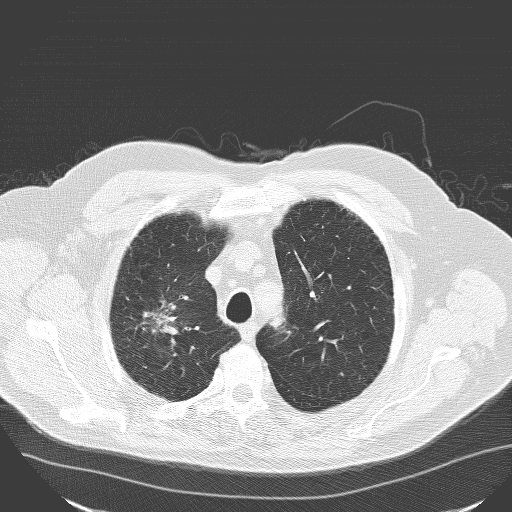
Low-dose screening chest CT, axial slice. First (baseline) screen. Lung window (W 1500 / L -600 HU). 3.2 mm slice thickness. 120 kVp. Slice 131 of 160 in the series. 512 × 512 image matrix. Male, age 71 years at enrolment. Current smoker at enrolment.
Expert-annotated lung lesion, bounding box (x1, y1, x2, y2) in pixels: (114, 277, 190, 355). The exam's reader record, not a measurement of the box and not confirmed to be the same lesion: non-calcified nodule or mass ≥4 mm, right upper lobe, 30 × 25 mm, spiculated (stellate) margins, soft tissue attenuation. Participant outcome: lung cancer diagnosed 182 days after this screen — squamous cell carcinoma, NOS, right upper lobe, poorly differentiated (G3), stage IA (AJCC 6th edition), 30 mm at pathology.